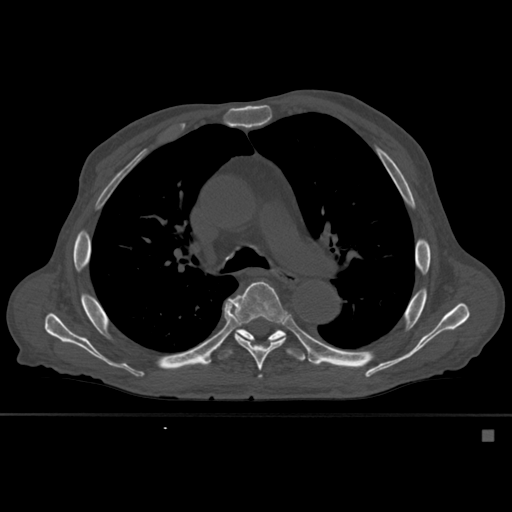
CT including the spine, one axial slice; position 380 of 527 along the scan axis; bone window (W 1800 / L 400 HU); 1.5 mm slice thickness; 512 × 512 image matrix, field of view 373 × 373 mm. Patient: male, 78 years. From the clinical record (not read from this slice): primary cancer: prostate.
Structures marked on this image (semi-automatically segmented with operator editing):
- T5 vertebra: bounding box (x1, y1, x2, y2) in pixels: (259, 375, 262, 377)
- T6 vertebra: (225, 281, 289, 371)
- T7 vertebra: (212, 329, 306, 362)